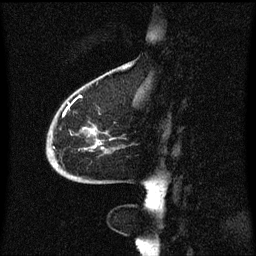
Breast MRI (dynamic contrast-enhanced), one sagittal slice. Slice 19 of 60 in the series (ordered by position). Dynamic contrast-enhanced series, image 2 of 3 at this slice position (ordered by acquisition). 1.5 T. TE 4.2 ms, TR 8.4 ms. 2 mm slice thickness. 256 × 256 image matrix, field of view 200 × 200 mm. Patient: female, 68 years. Case-level facts recorded for this patient, not image findings: setting: breast cancer imaged before/during neoadjuvant chemotherapy; receptor status: triple-negative.
Structures marked on this image (semi-automatically segmented with operator editing):
- analysis volume of interest (the breast-tissue region the enhancement analysis was run in; not a lesion): bounding box [x1, y1, x2, y2] px = [48, 94, 126, 173]
- tumour enhancement mask (voxels above the 70 % enhancement threshold inside the analysis volume of interest): [54, 96, 102, 167]